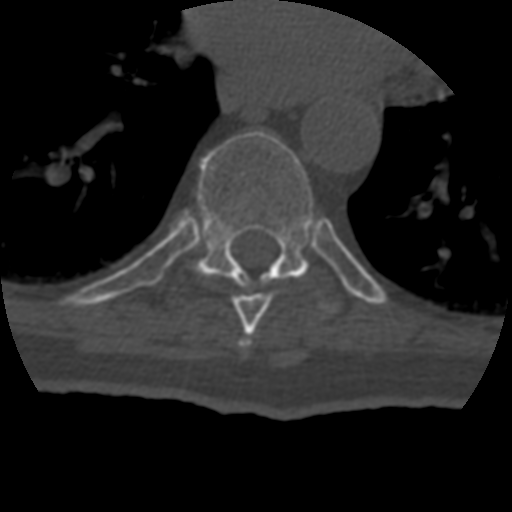
CT including the spine, one axial slice; position 248 of 399 along the scan axis; reconstruction kernel STANDARD; 120 kVp; bone window (W 1800 / L 400 HU); 1.25 mm slice thickness; 512 × 512 image matrix, field of view 160 × 160 mm. Patient age 69 years. From the clinical record (not read from this slice): primary cancer: prostate.
Structures marked on this image (semi-automatically segmented with operator editing):
- T7 vertebra: box from (x=240, y=340) to (x=251, y=346) px
- T8 vertebra: (x=233, y=293)–(x=273, y=336)
- T9 vertebra: (x=168, y=131)–(x=343, y=315)